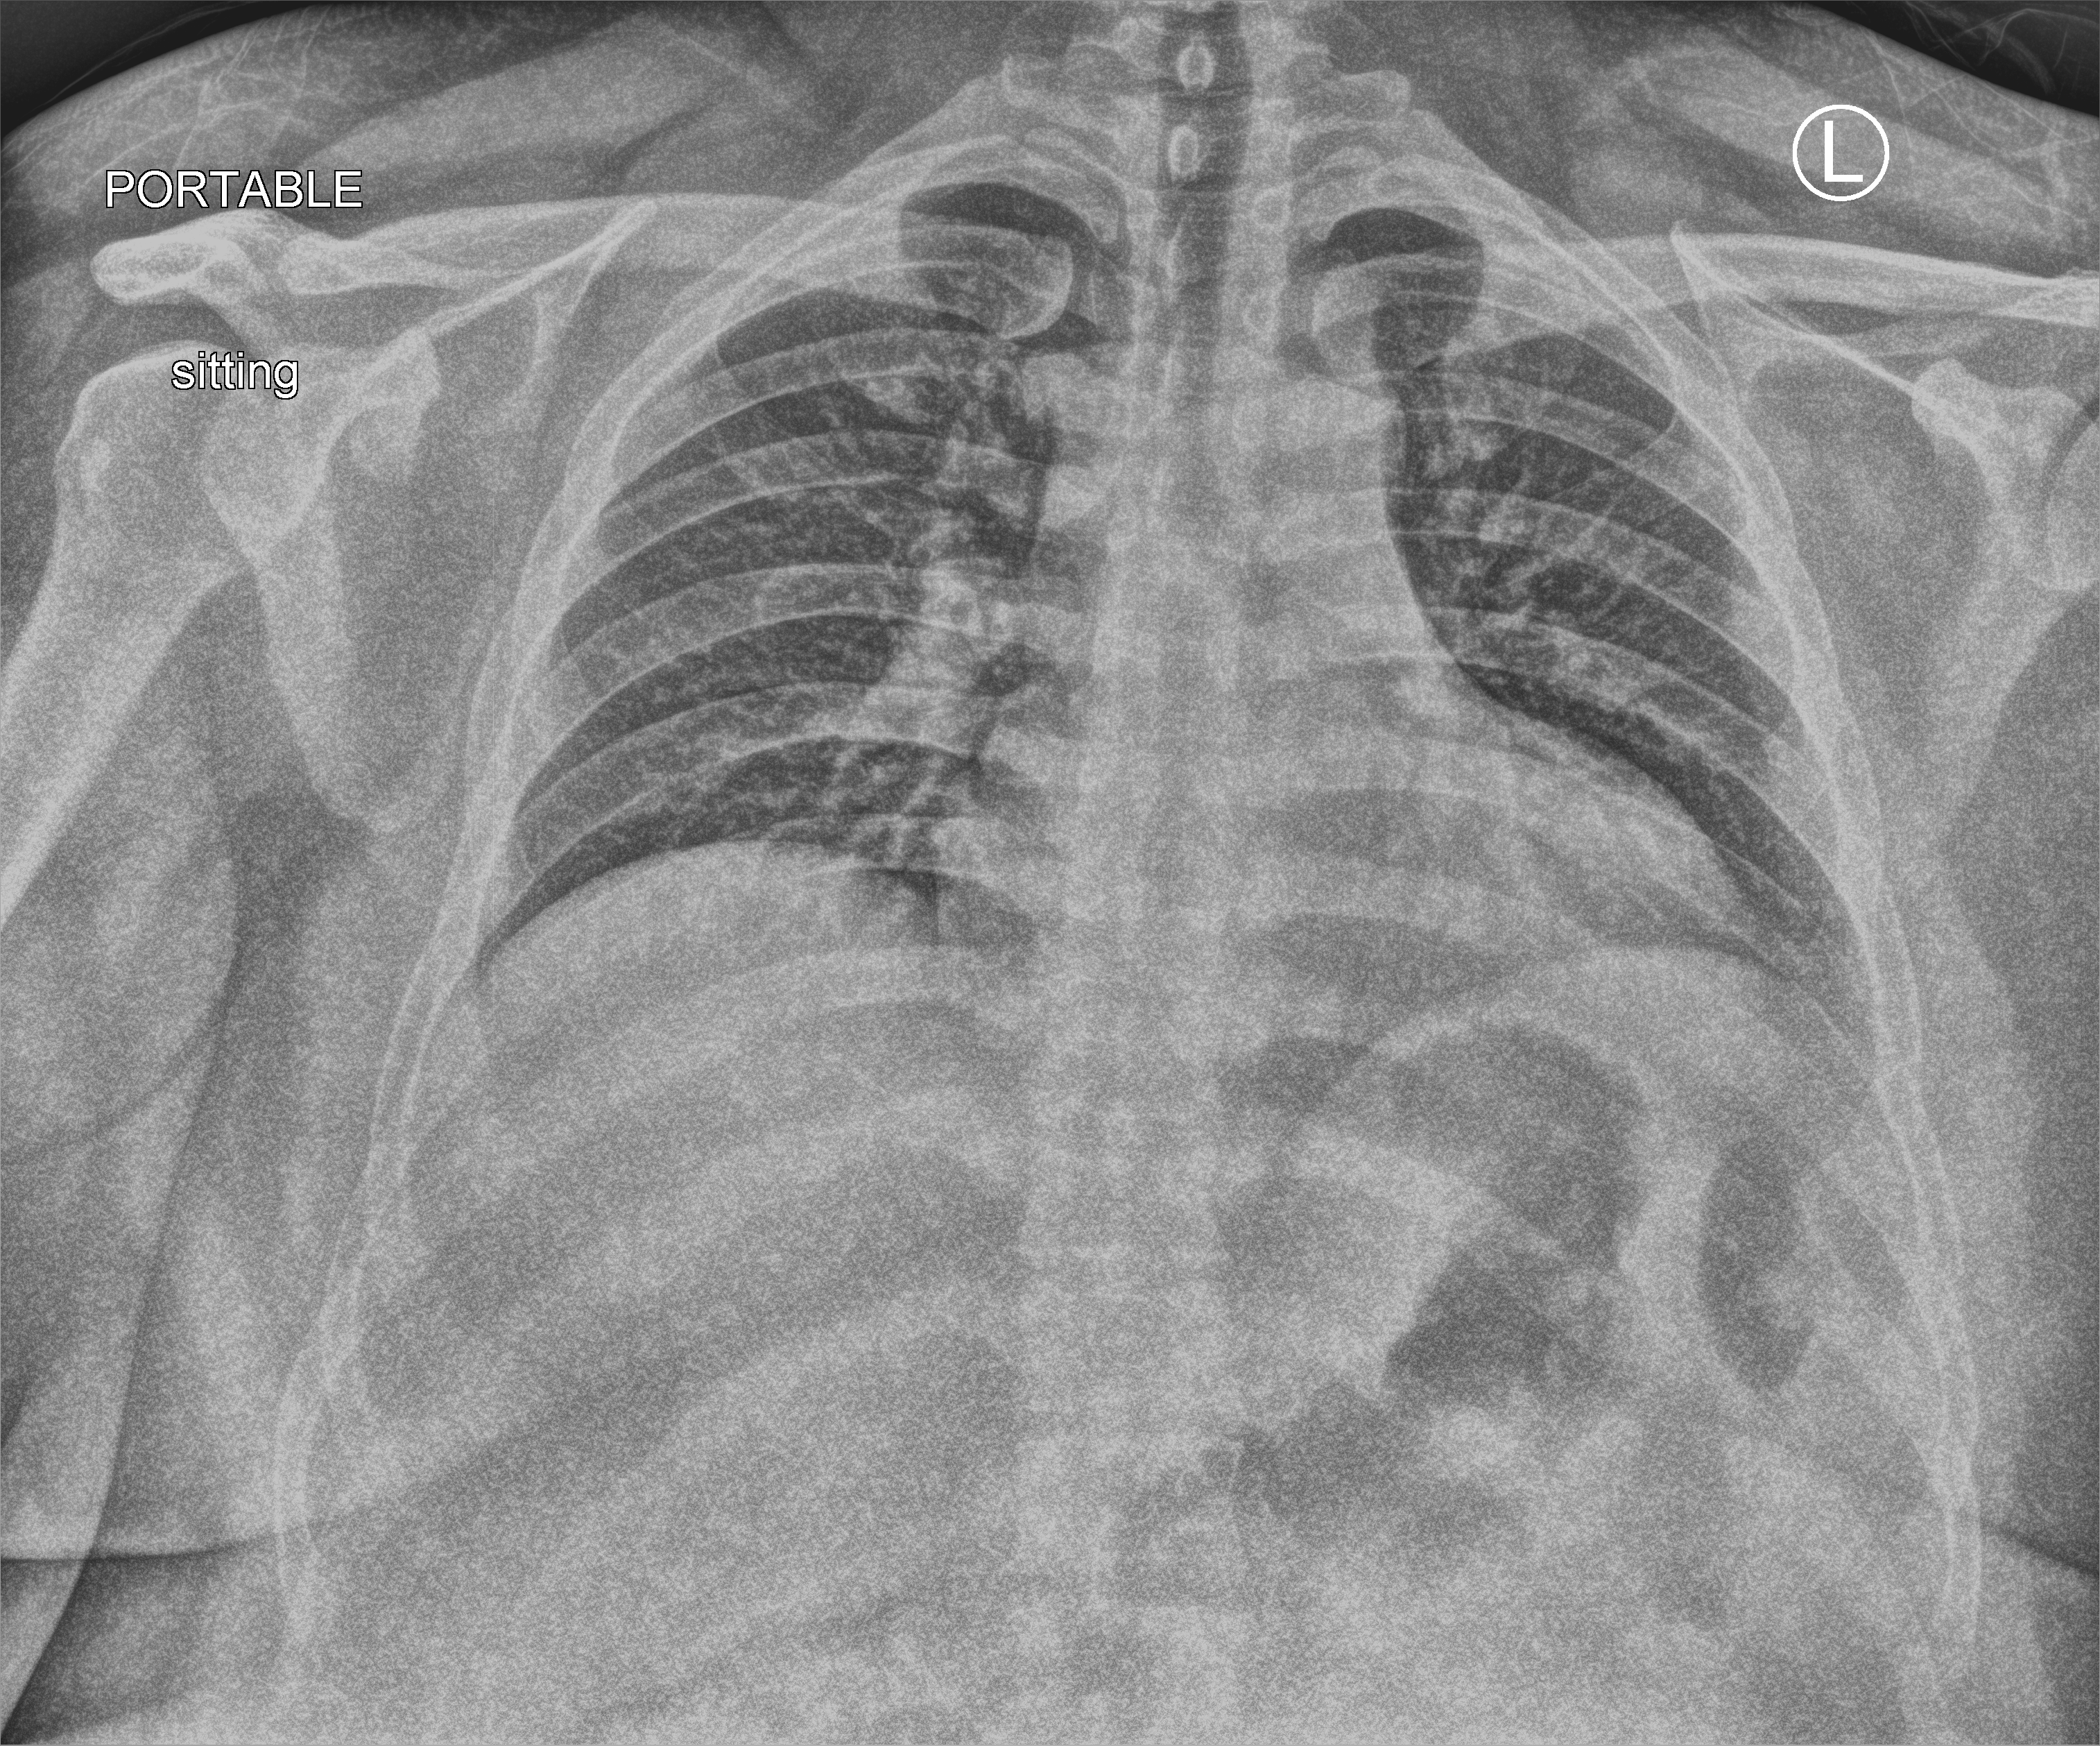
Portable chest radiograph, anteroposterior (AP) projection. Male patient hospitalised with COVID-19, age 18–59 years.
Hospital-stay facts (about this admission, not read from this image; timing relative to this image not recorded): admitted to intensive care during this hospital stay: no.